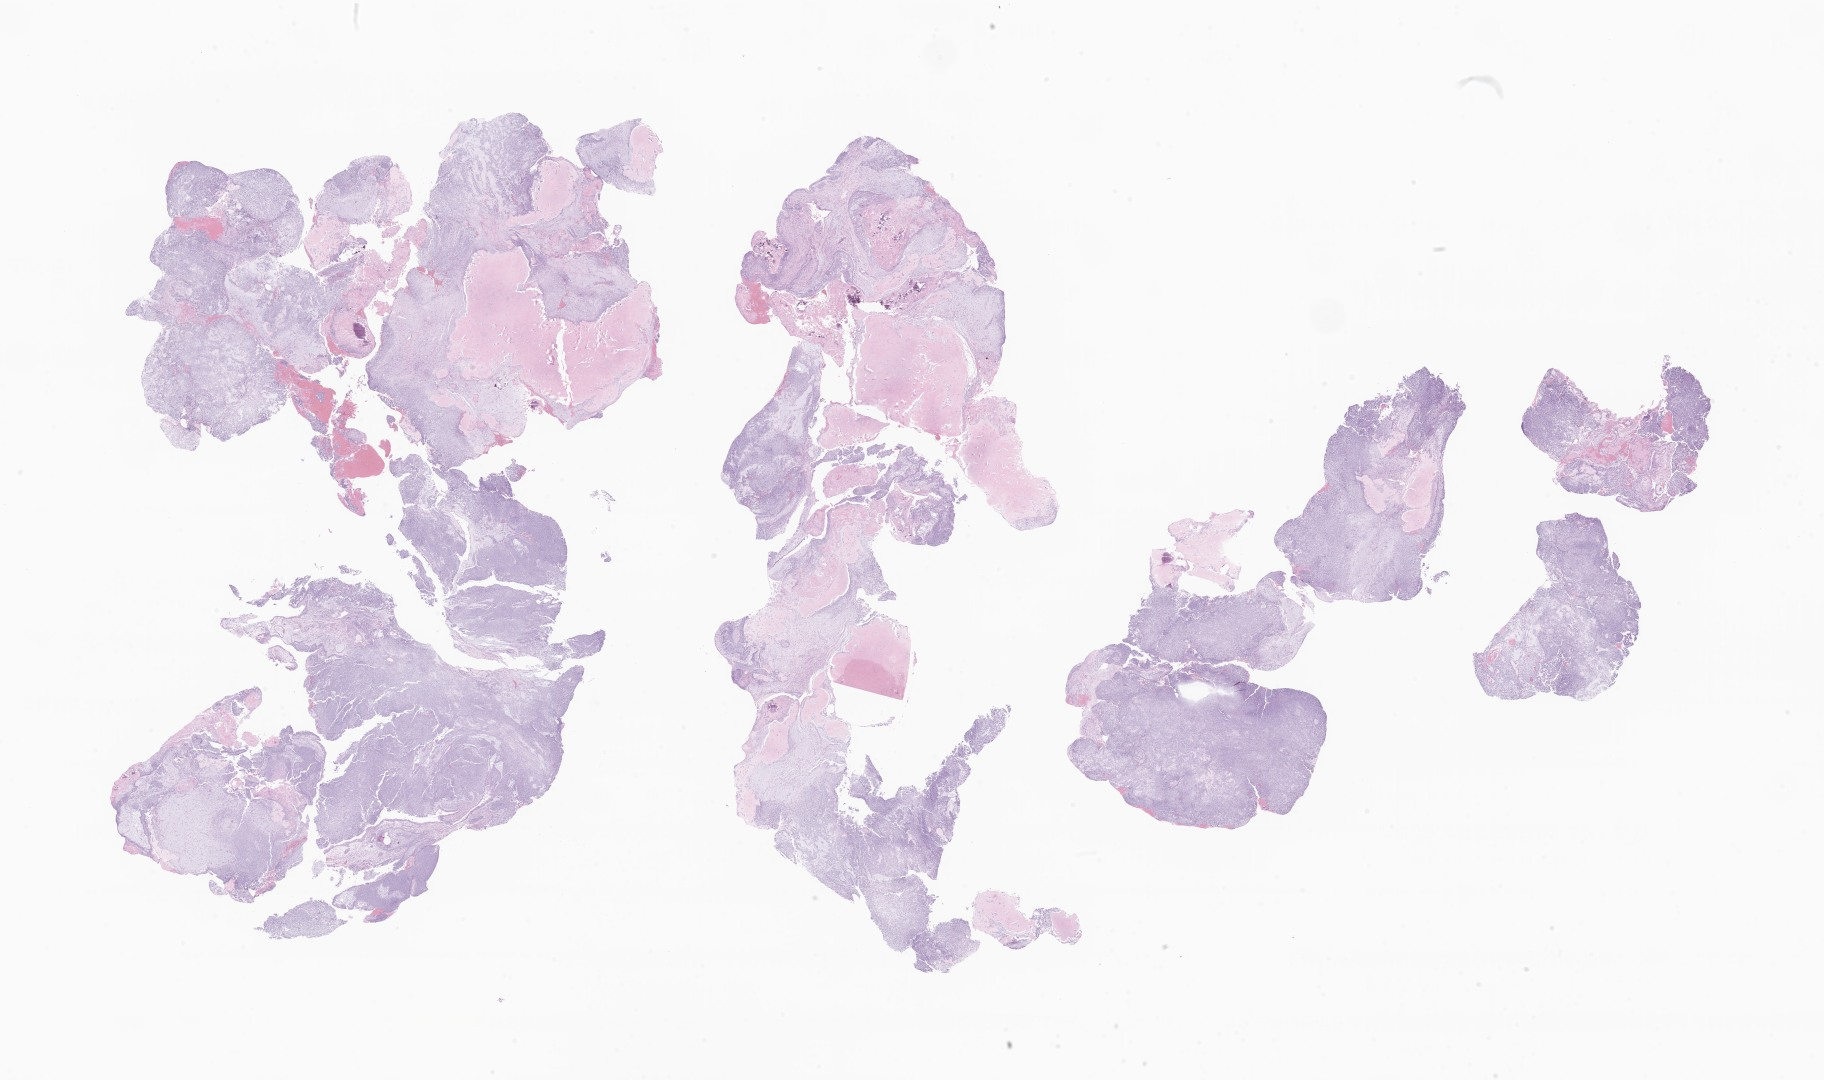
H&E whole-slide image of tumor tissue from the brain, low-resolution overview of the scanned area, about 30.8 x 18.2 mm, formalin-fixed paraffin-embedded section. Patient: male, age 727 days (about 2.0 years).
- diagnosis: Craniopharyngioma, NOS